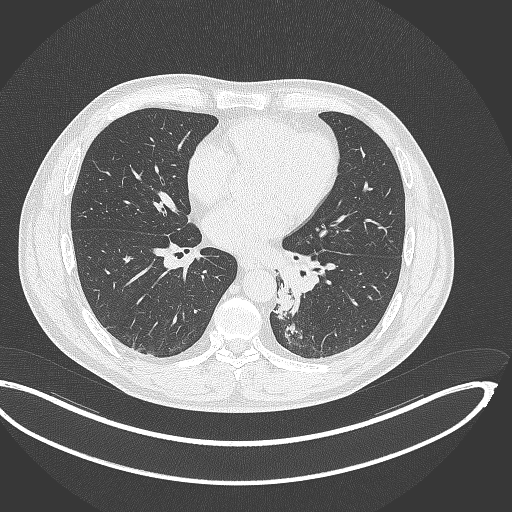
Chest CT, one axial slice; lung window (W 1500 / L -600 HU); 1 mm slice thickness; 512 × 512 image matrix. Male patient, age 50 years. From the clinical record (not read from this slice): clinical TNM (as recorded): T2a N3 M0.
Annotated regions visible in this slice (bounding box drawn by a radiologist):
- lung tumour (recorded histology: squamous cell carcinoma): bounding box [x1, y1, x2, y2] px = [271, 282, 295, 318]